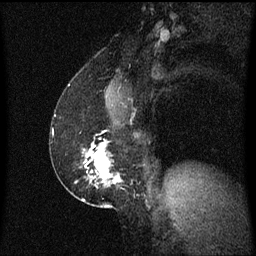
Breast MRI (dynamic contrast-enhanced), one sagittal slice. Slice 36 of 60 in the series (ordered by position). Dynamic contrast-enhanced series, image 2 of 3 at this slice position (ordered by acquisition). 1.5 T. TE 4.2 ms, TR 8.4 ms. 2 mm slice thickness. 256 × 256 image matrix. Female patient, age 52 years. From the clinical record (not read from this slice): setting: breast cancer imaged before/during neoadjuvant chemotherapy; receptor status: HER2-positive.
Annotated regions visible in this slice (semi-automatically segmented with operator editing):
- analysis volume of interest (the breast-tissue region the enhancement analysis was run in; not a lesion): bounding box <62,142,122,203> (left, top, right, bottom; pixels)
- tumour enhancement mask (voxels above the 70 % enhancement threshold inside the analysis volume of interest): <86,142,121,187>